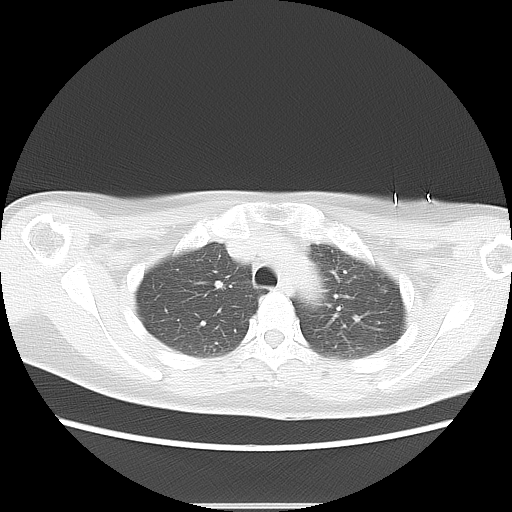
Chest CT, one axial slice; slice 10 of 16 in the series (ordered by position); lung window (W 1500 / L -600 HU); 512 × 512 image matrix, field of view 350 × 350 mm. Female patient, age 42 years. Case-level facts recorded for this patient, not image findings: clinical TNM (as recorded): Tis N0 M0.
Outlined on this slice (rectangle marked by the reading radiologist):
- lung tumour (recorded histology: adenocarcinoma): bounding box <376,281,389,300> (left, top, right, bottom; pixels)